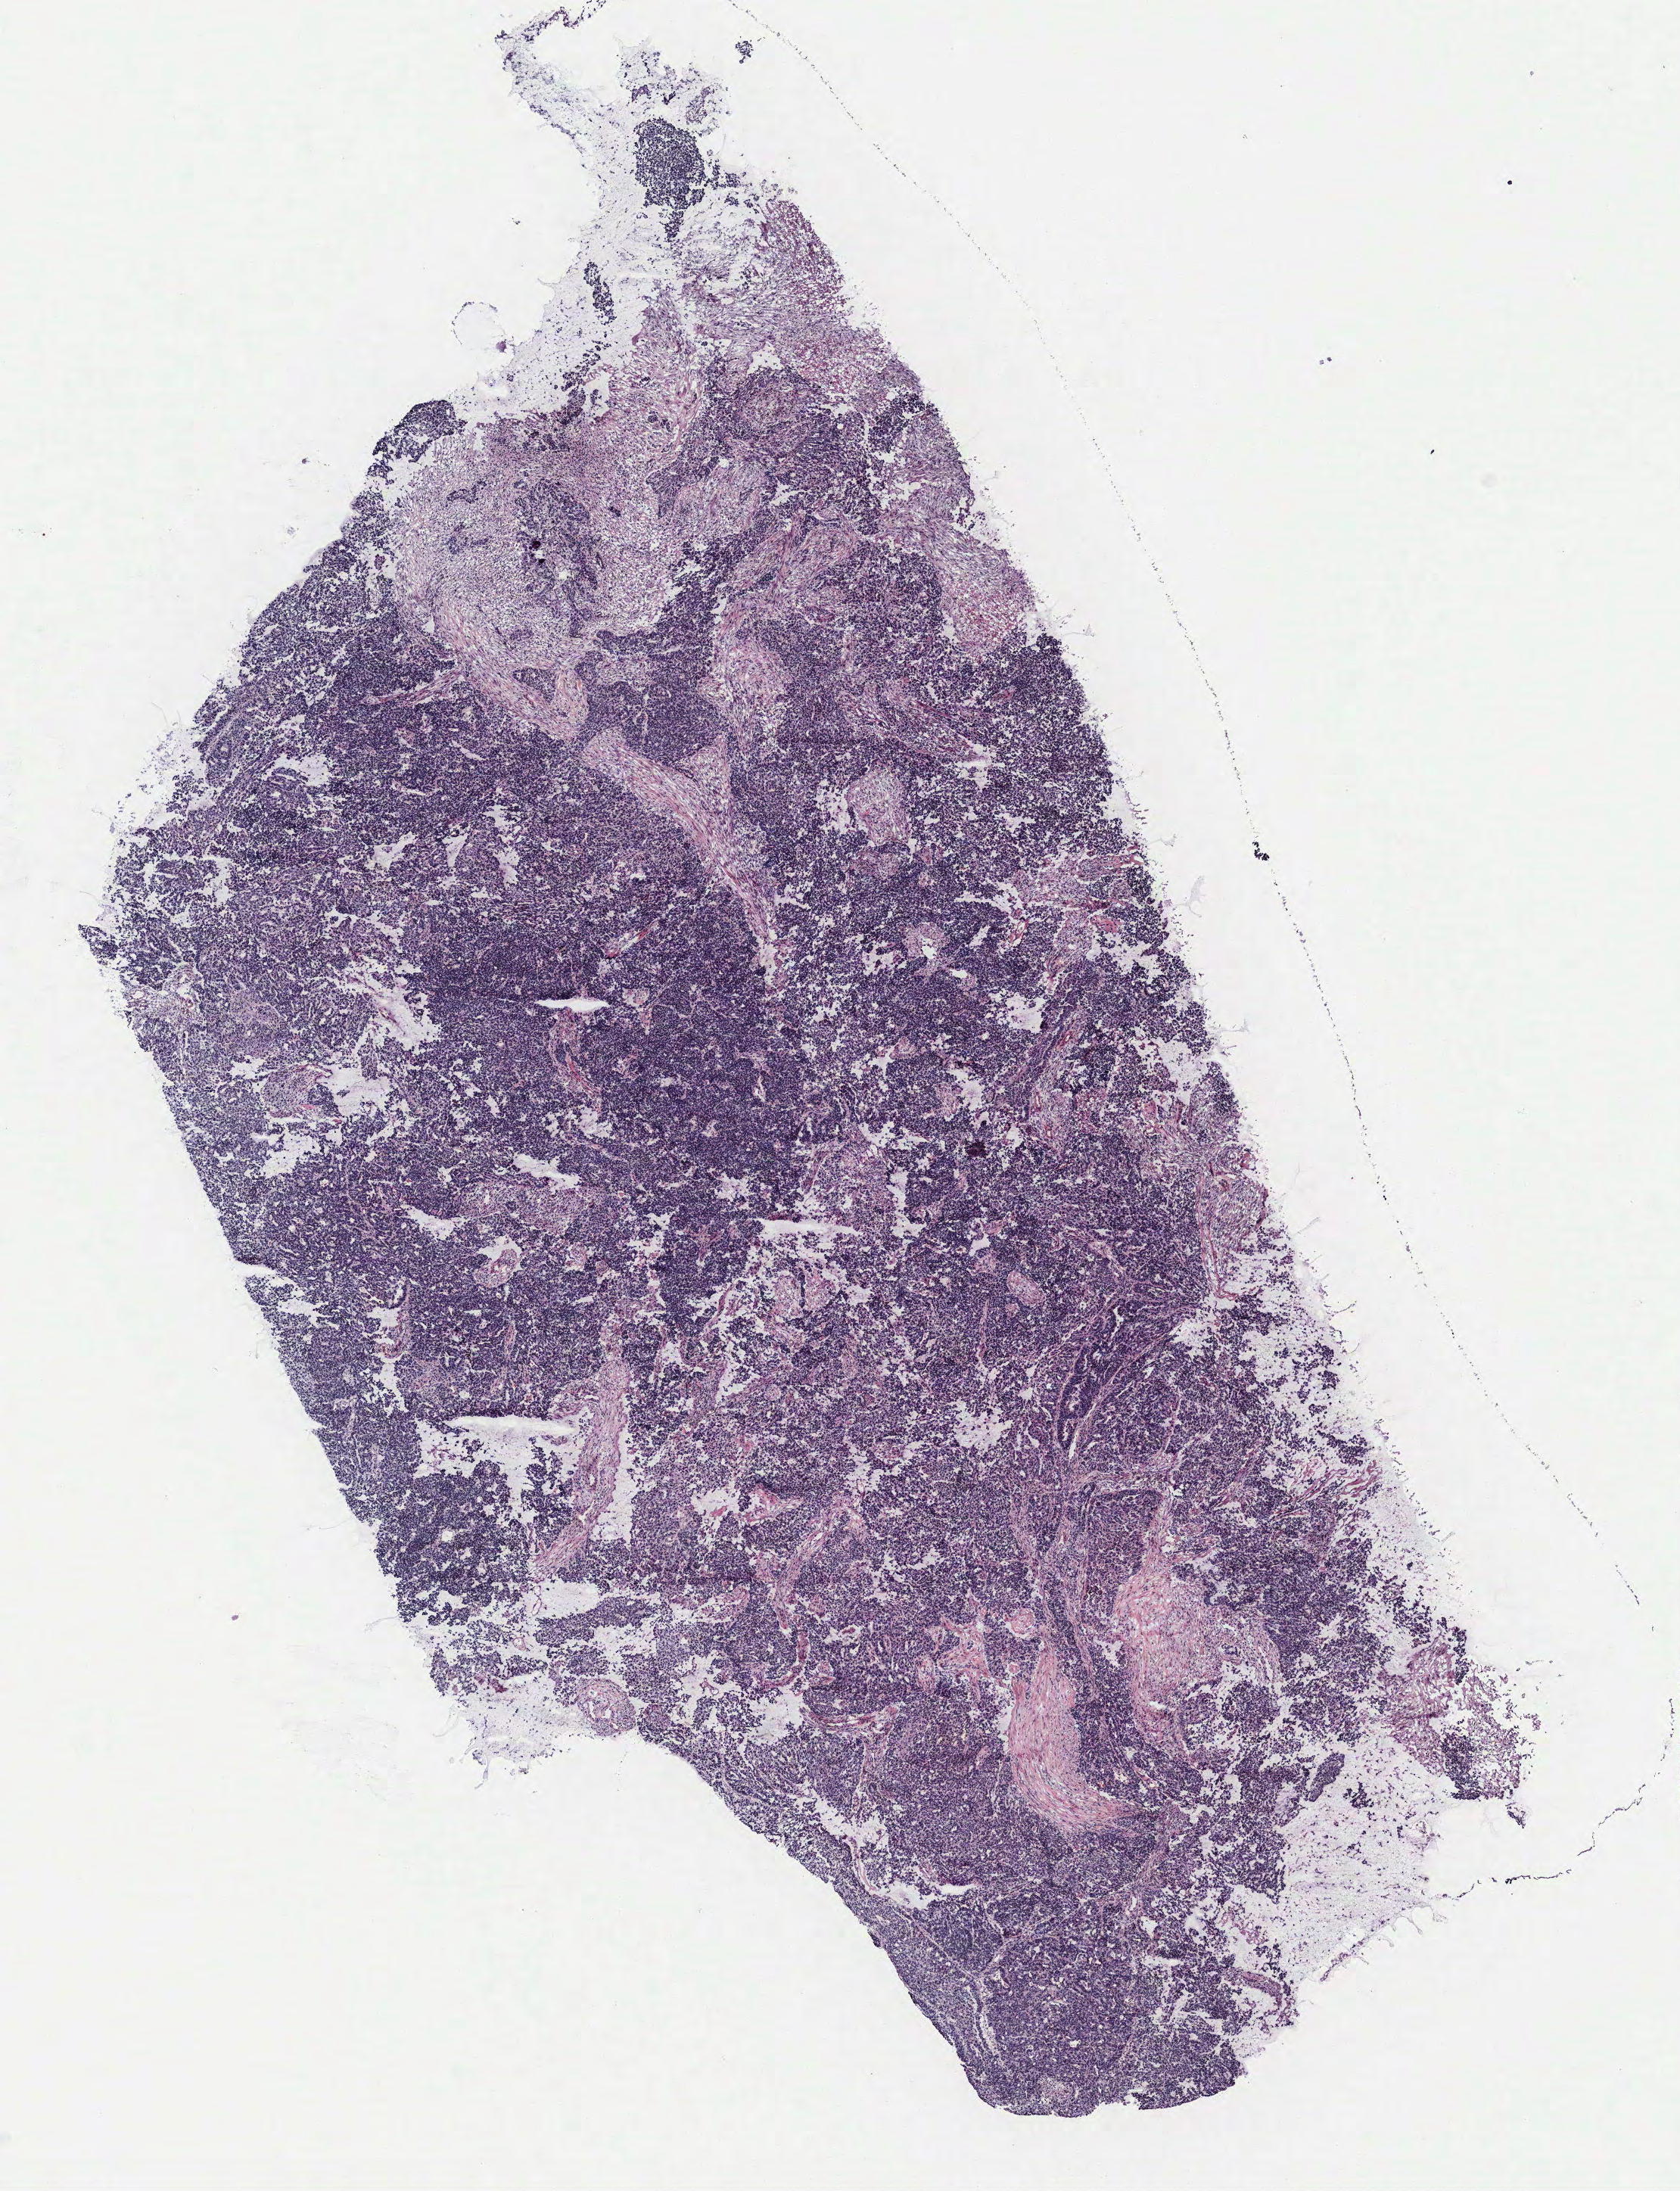
Whole-slide histology image, H&E-stained, a low-resolution overview of the entire scanned area, about 8.9 x 11.6 mm (slide scanned at 40x); ovary, tumour tissue. Patient: female, age 44 years.
• diagnosis: Serous adenocarcinoma, NOS
• primary tumour site (as recorded): ovary